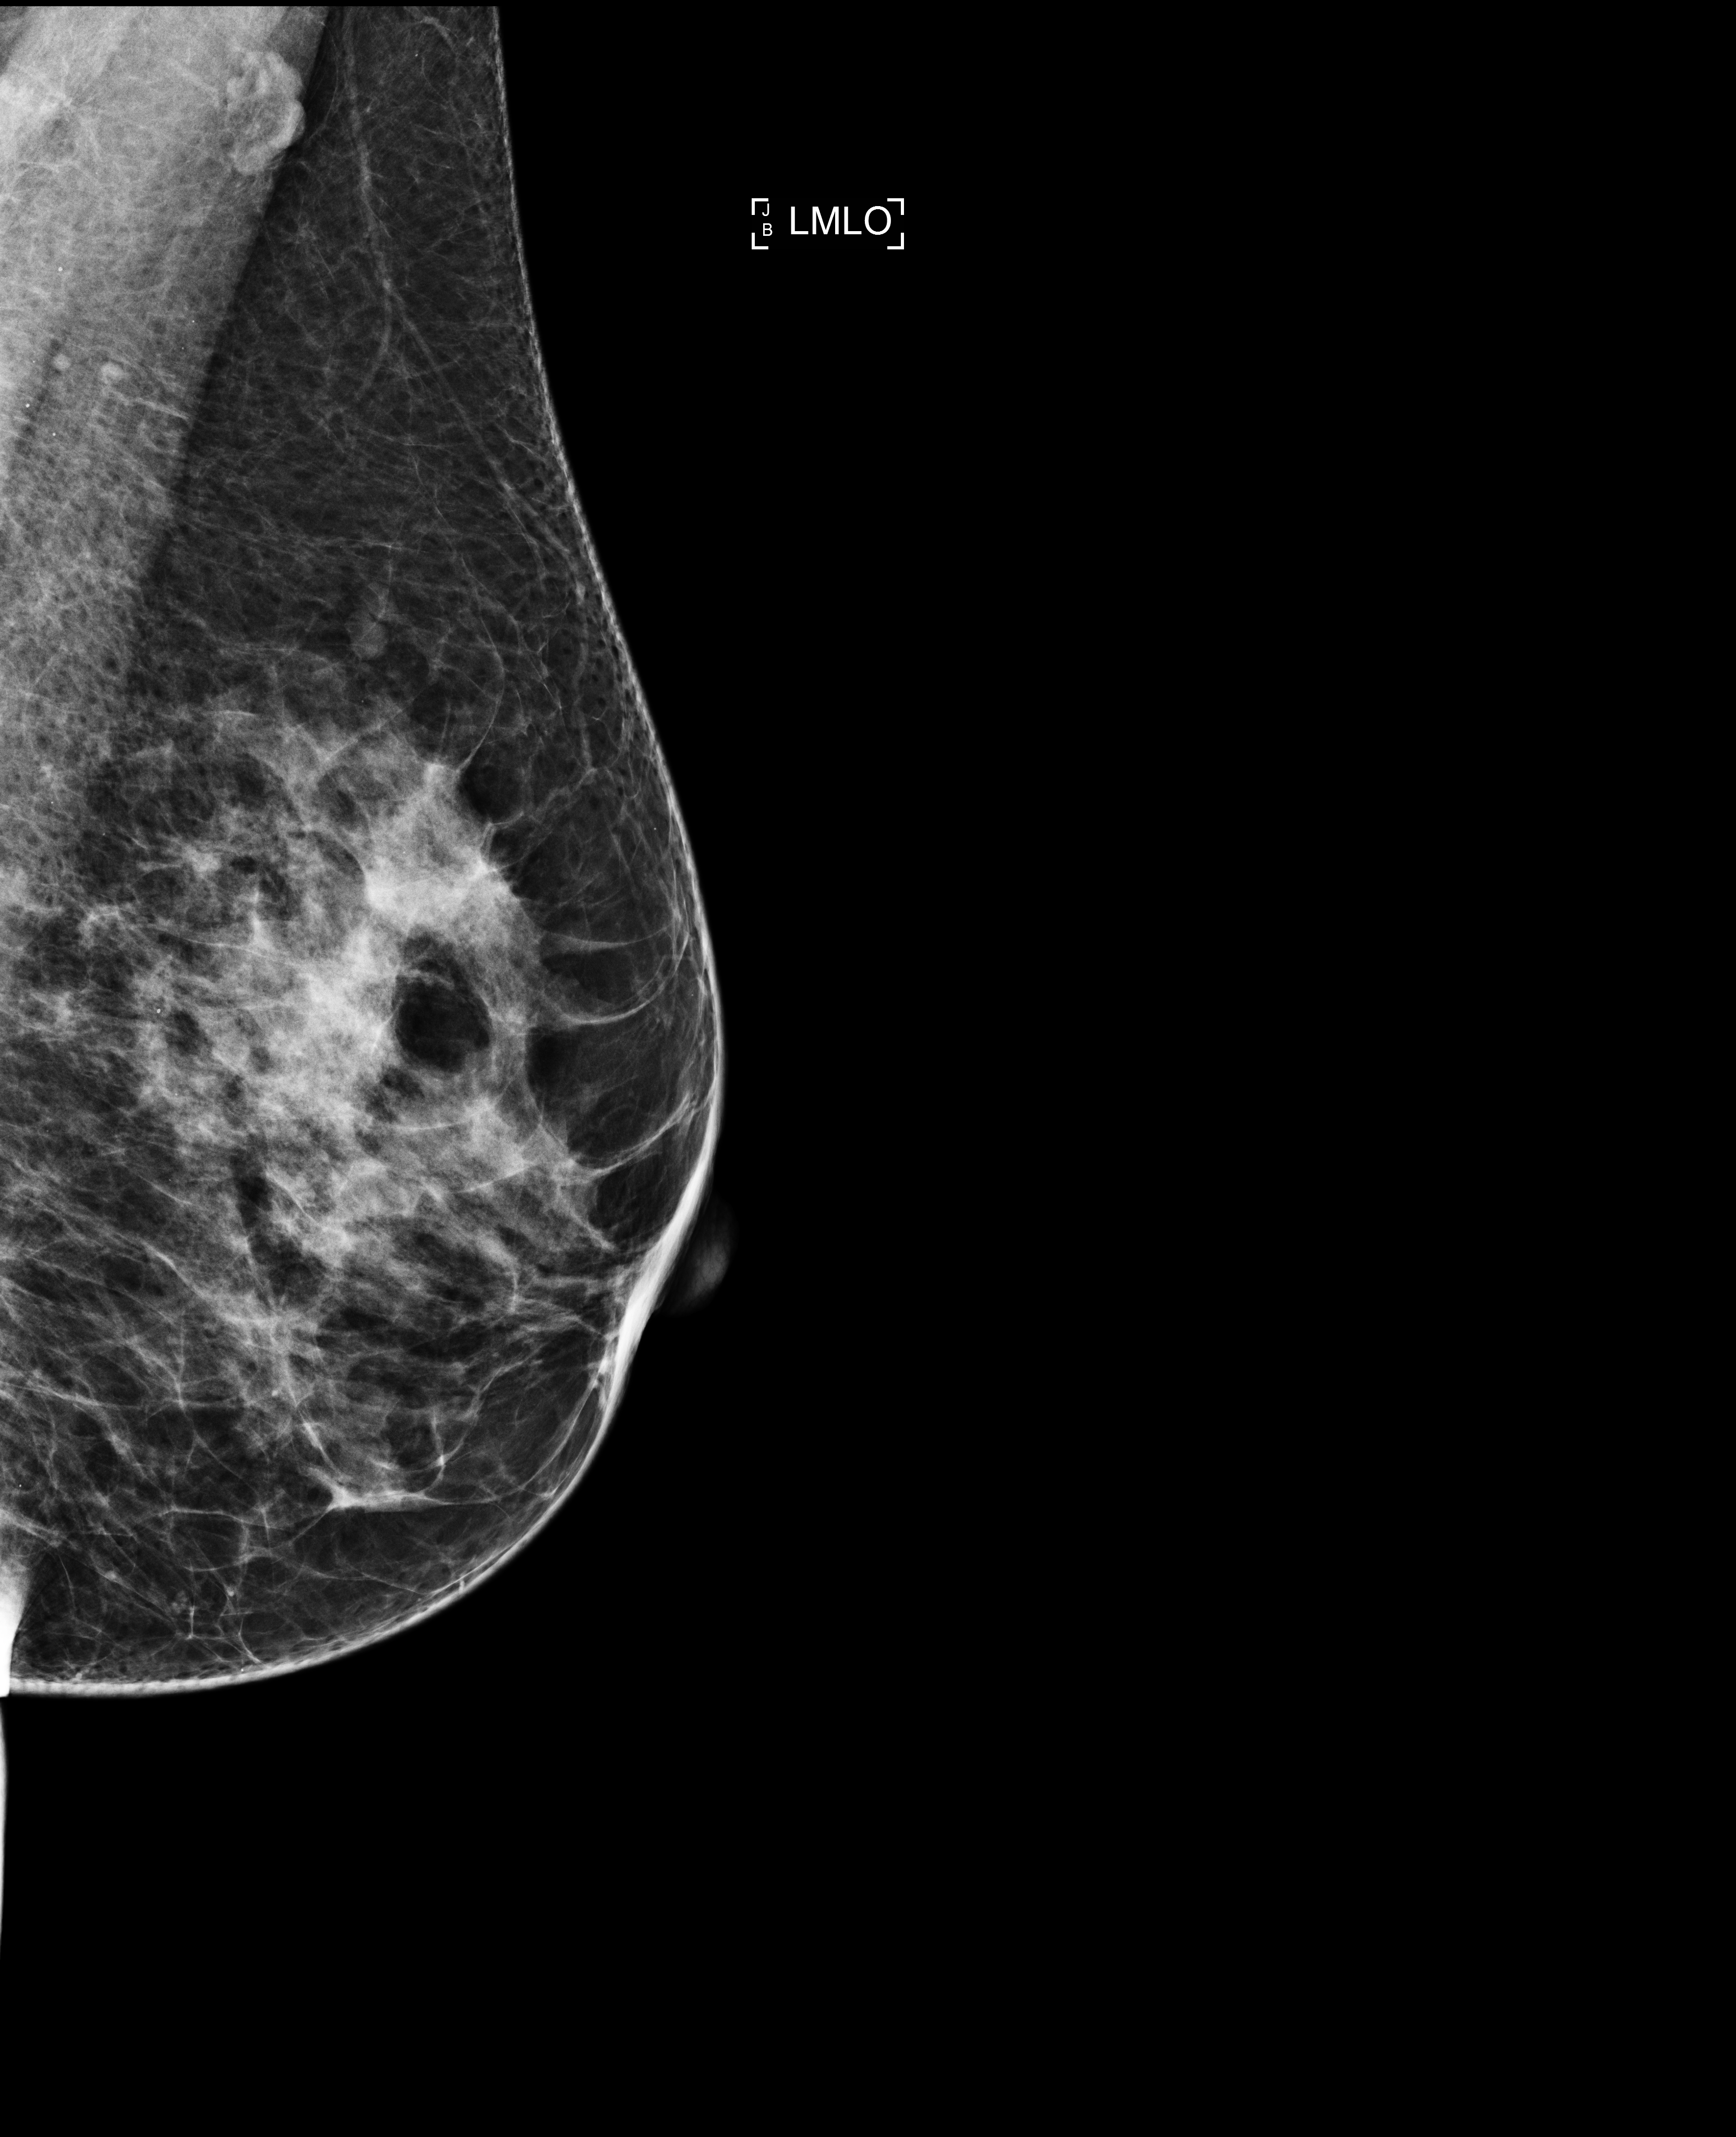
Full-field digital mammogram (FFDM), left breast, mediolateral oblique (MLO) view, annual screening mammography examination, compressed breast thickness 57 mm, system: Selenia Dimensions. Female patient, age 59 years.
Final BI-RADS category for the screening round (tomosynthesis exam, both breasts): category 1.